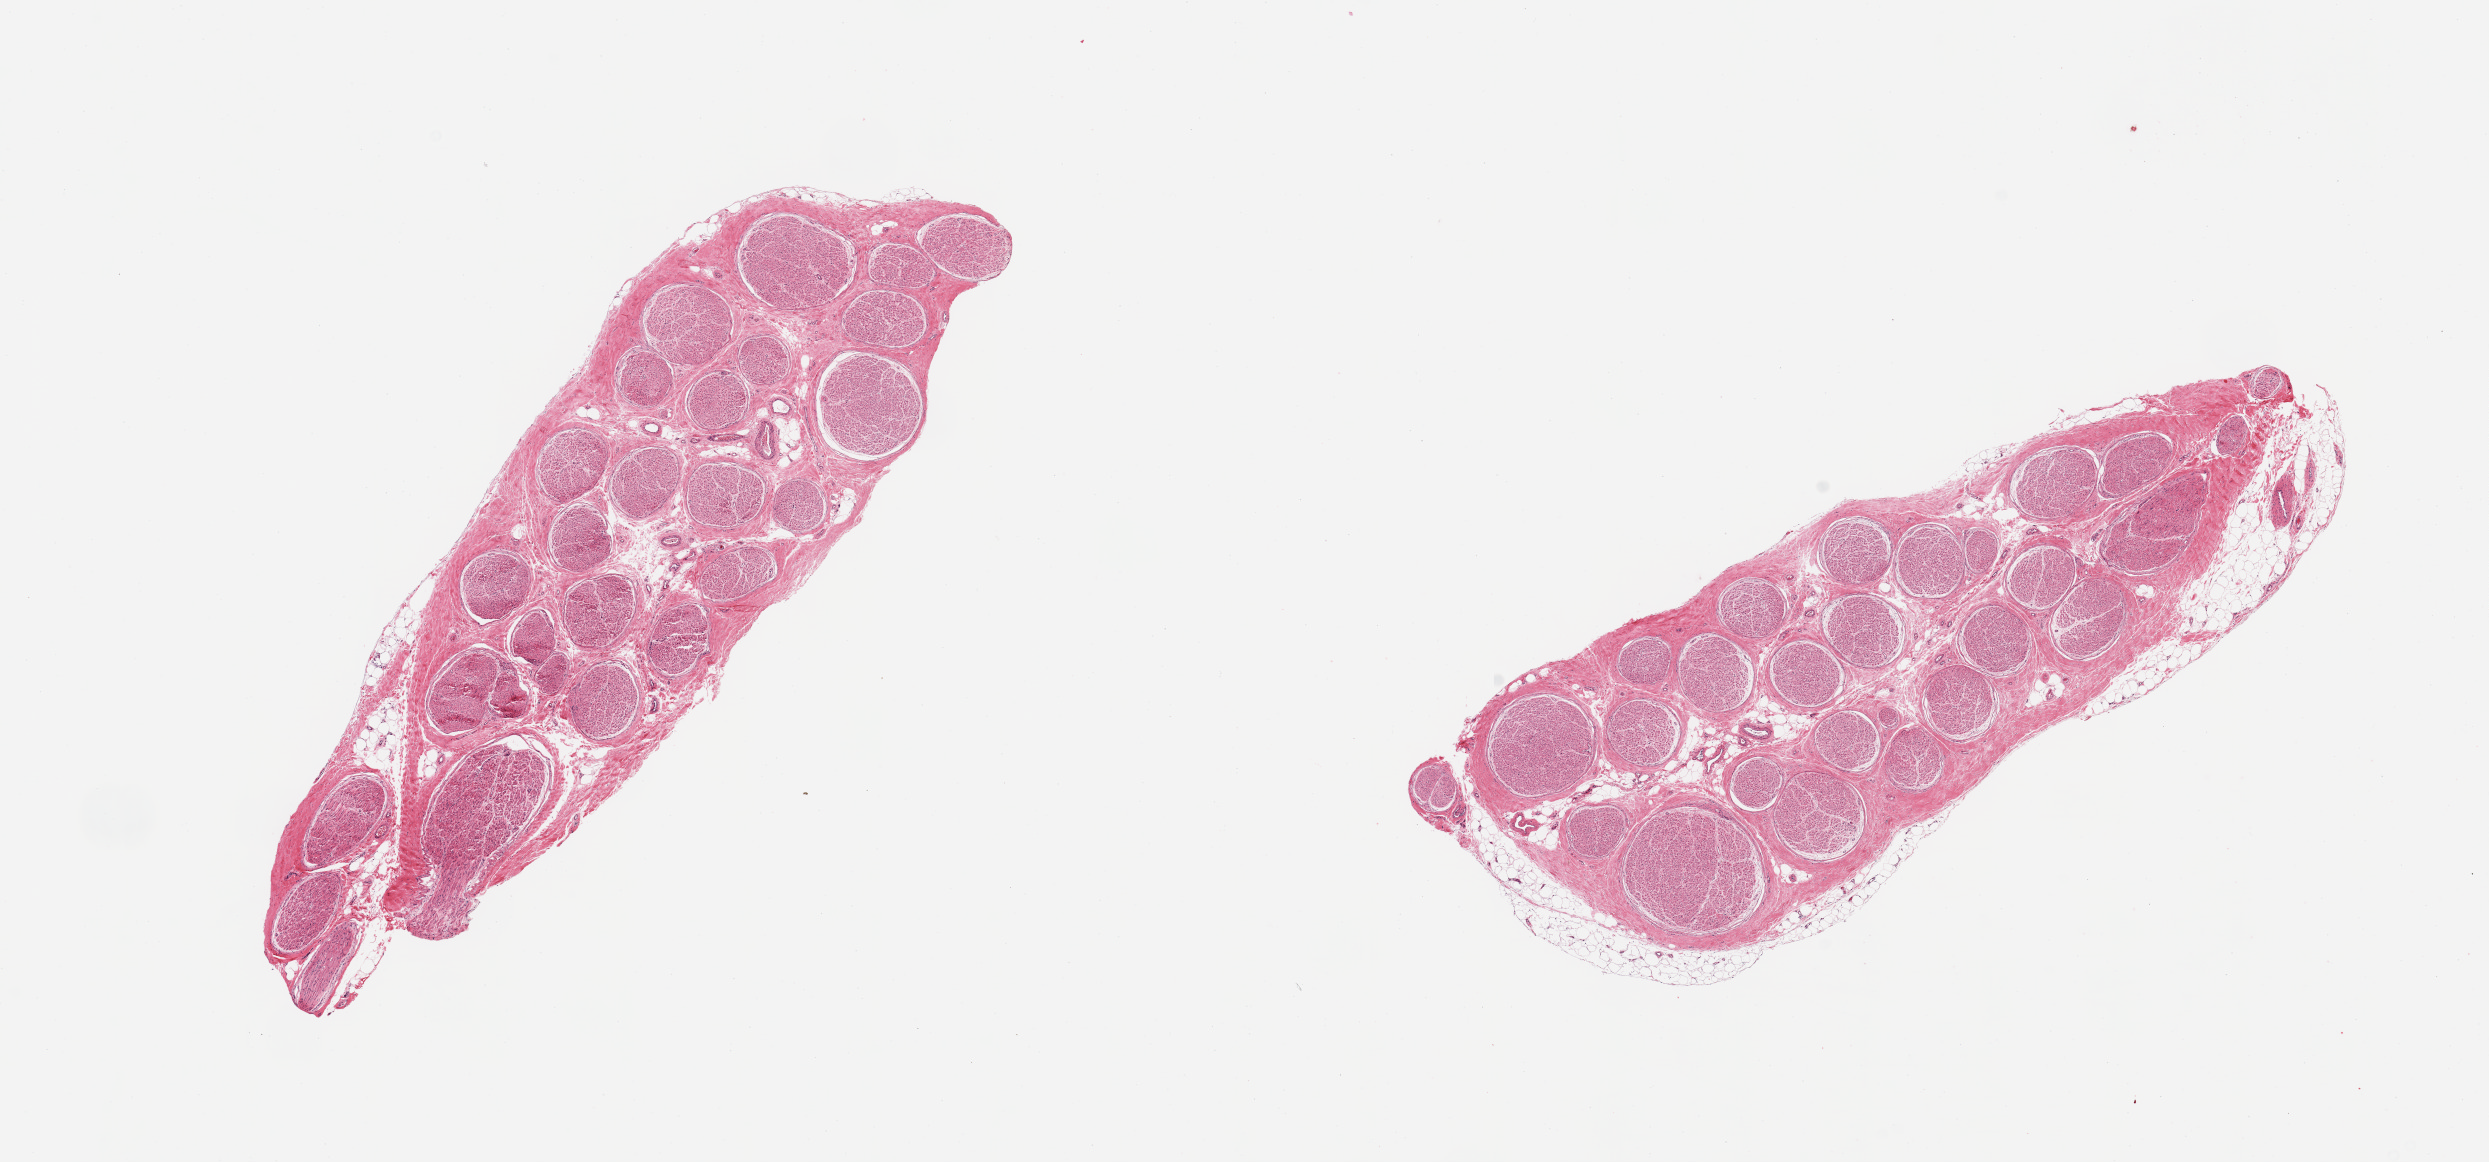
Whole-slide image, haematoxylin and eosin stain — whole scanned area (about 19.7 x 9.2 mm) shown as a low-resolution overview; PAXgene-fixed paraffin-embedded (PFPE) section; sampled site (target tissue): tibial nerve; tissue donor sample. Donor: male.
* review note (as recorded): 2 pieces; includes small portion of fat, up to 10% in 1 piece